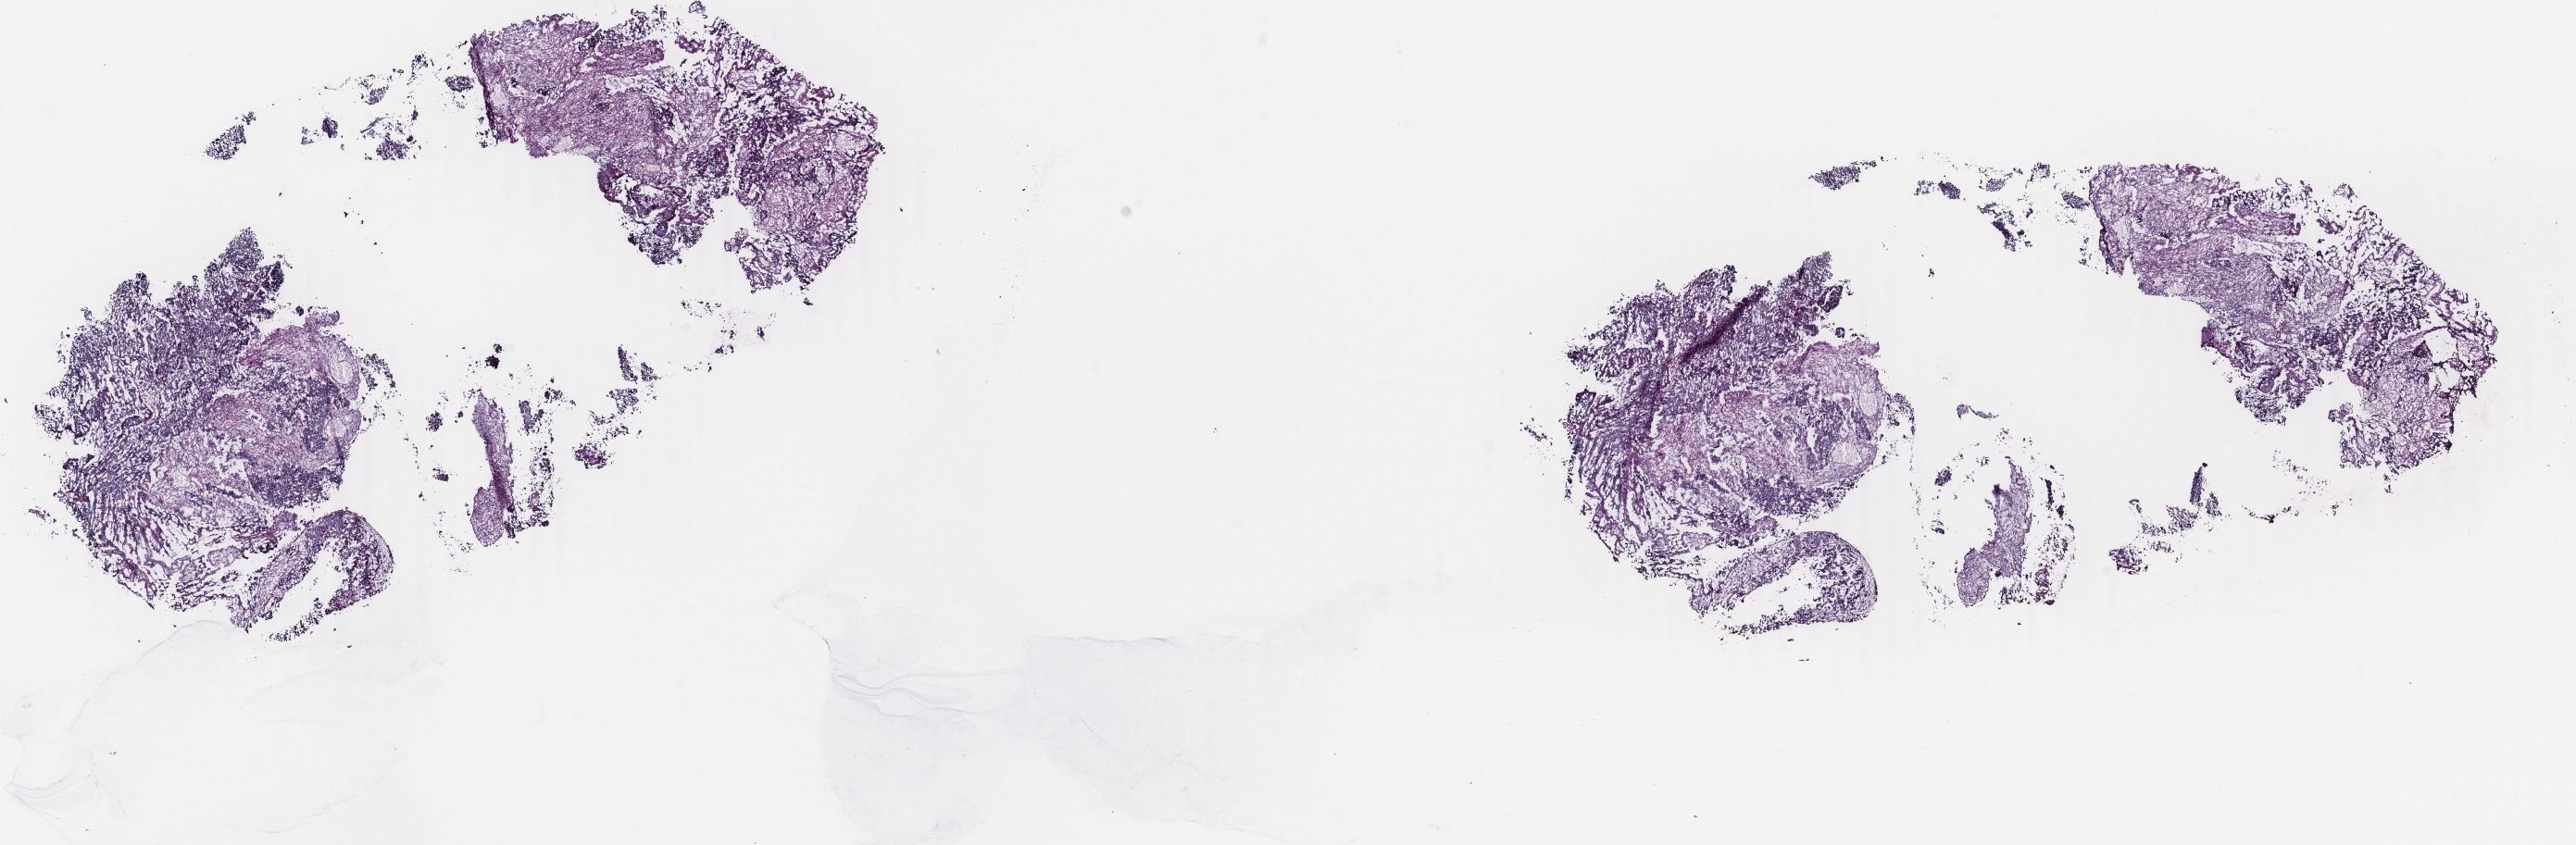
Whole-slide histology image, Hematoxylin and eosin (H&E) stained, a low-resolution overview of the entire scanned area, about 22.1 x 7.3 mm (from a 40x scan); frozen section from the top of the tissue portion; uterus, primary tumour sample. Female patient; age at initial diagnosis 74 years. Histologic grade: G3 (poorly differentiated). Composition of this section per pathologist review: tumour cells 50%, tumour nuclei 70%, normal cells 0%, stromal cells 30%, necrosis 20%. Inflammatory infiltration, as recorded: lymphocyte infiltration 10%, monocyte infiltration 0%, neutrophil infiltration 10%.
Histologic diagnosis: Endometrioid adenocarcinoma, NOS (endometrium). FIGO stage: IVB.